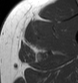
MRI of an extremity soft-tissue mass, one axial slice; slice 36 of 43 in the series (ordered by position); MR volume resampled by the dataset authors to the PET/CT grid (not the native acquisition matrix); 3.27 mm slice thickness; 78 × 83 image matrix. Male patient. From the clinical record (not read from this slice): histological type: pleiomorphic leiomyosarcoma; grade: high; site of the primary tumour: left thigh.
Outlined on this slice (expert contour drawn on MRI and transferred to this co-registered scan by the dataset authors):
- gross tumour volume including surrounding oedema: bounding box <24,33,37,48> (left, top, right, bottom; pixels)